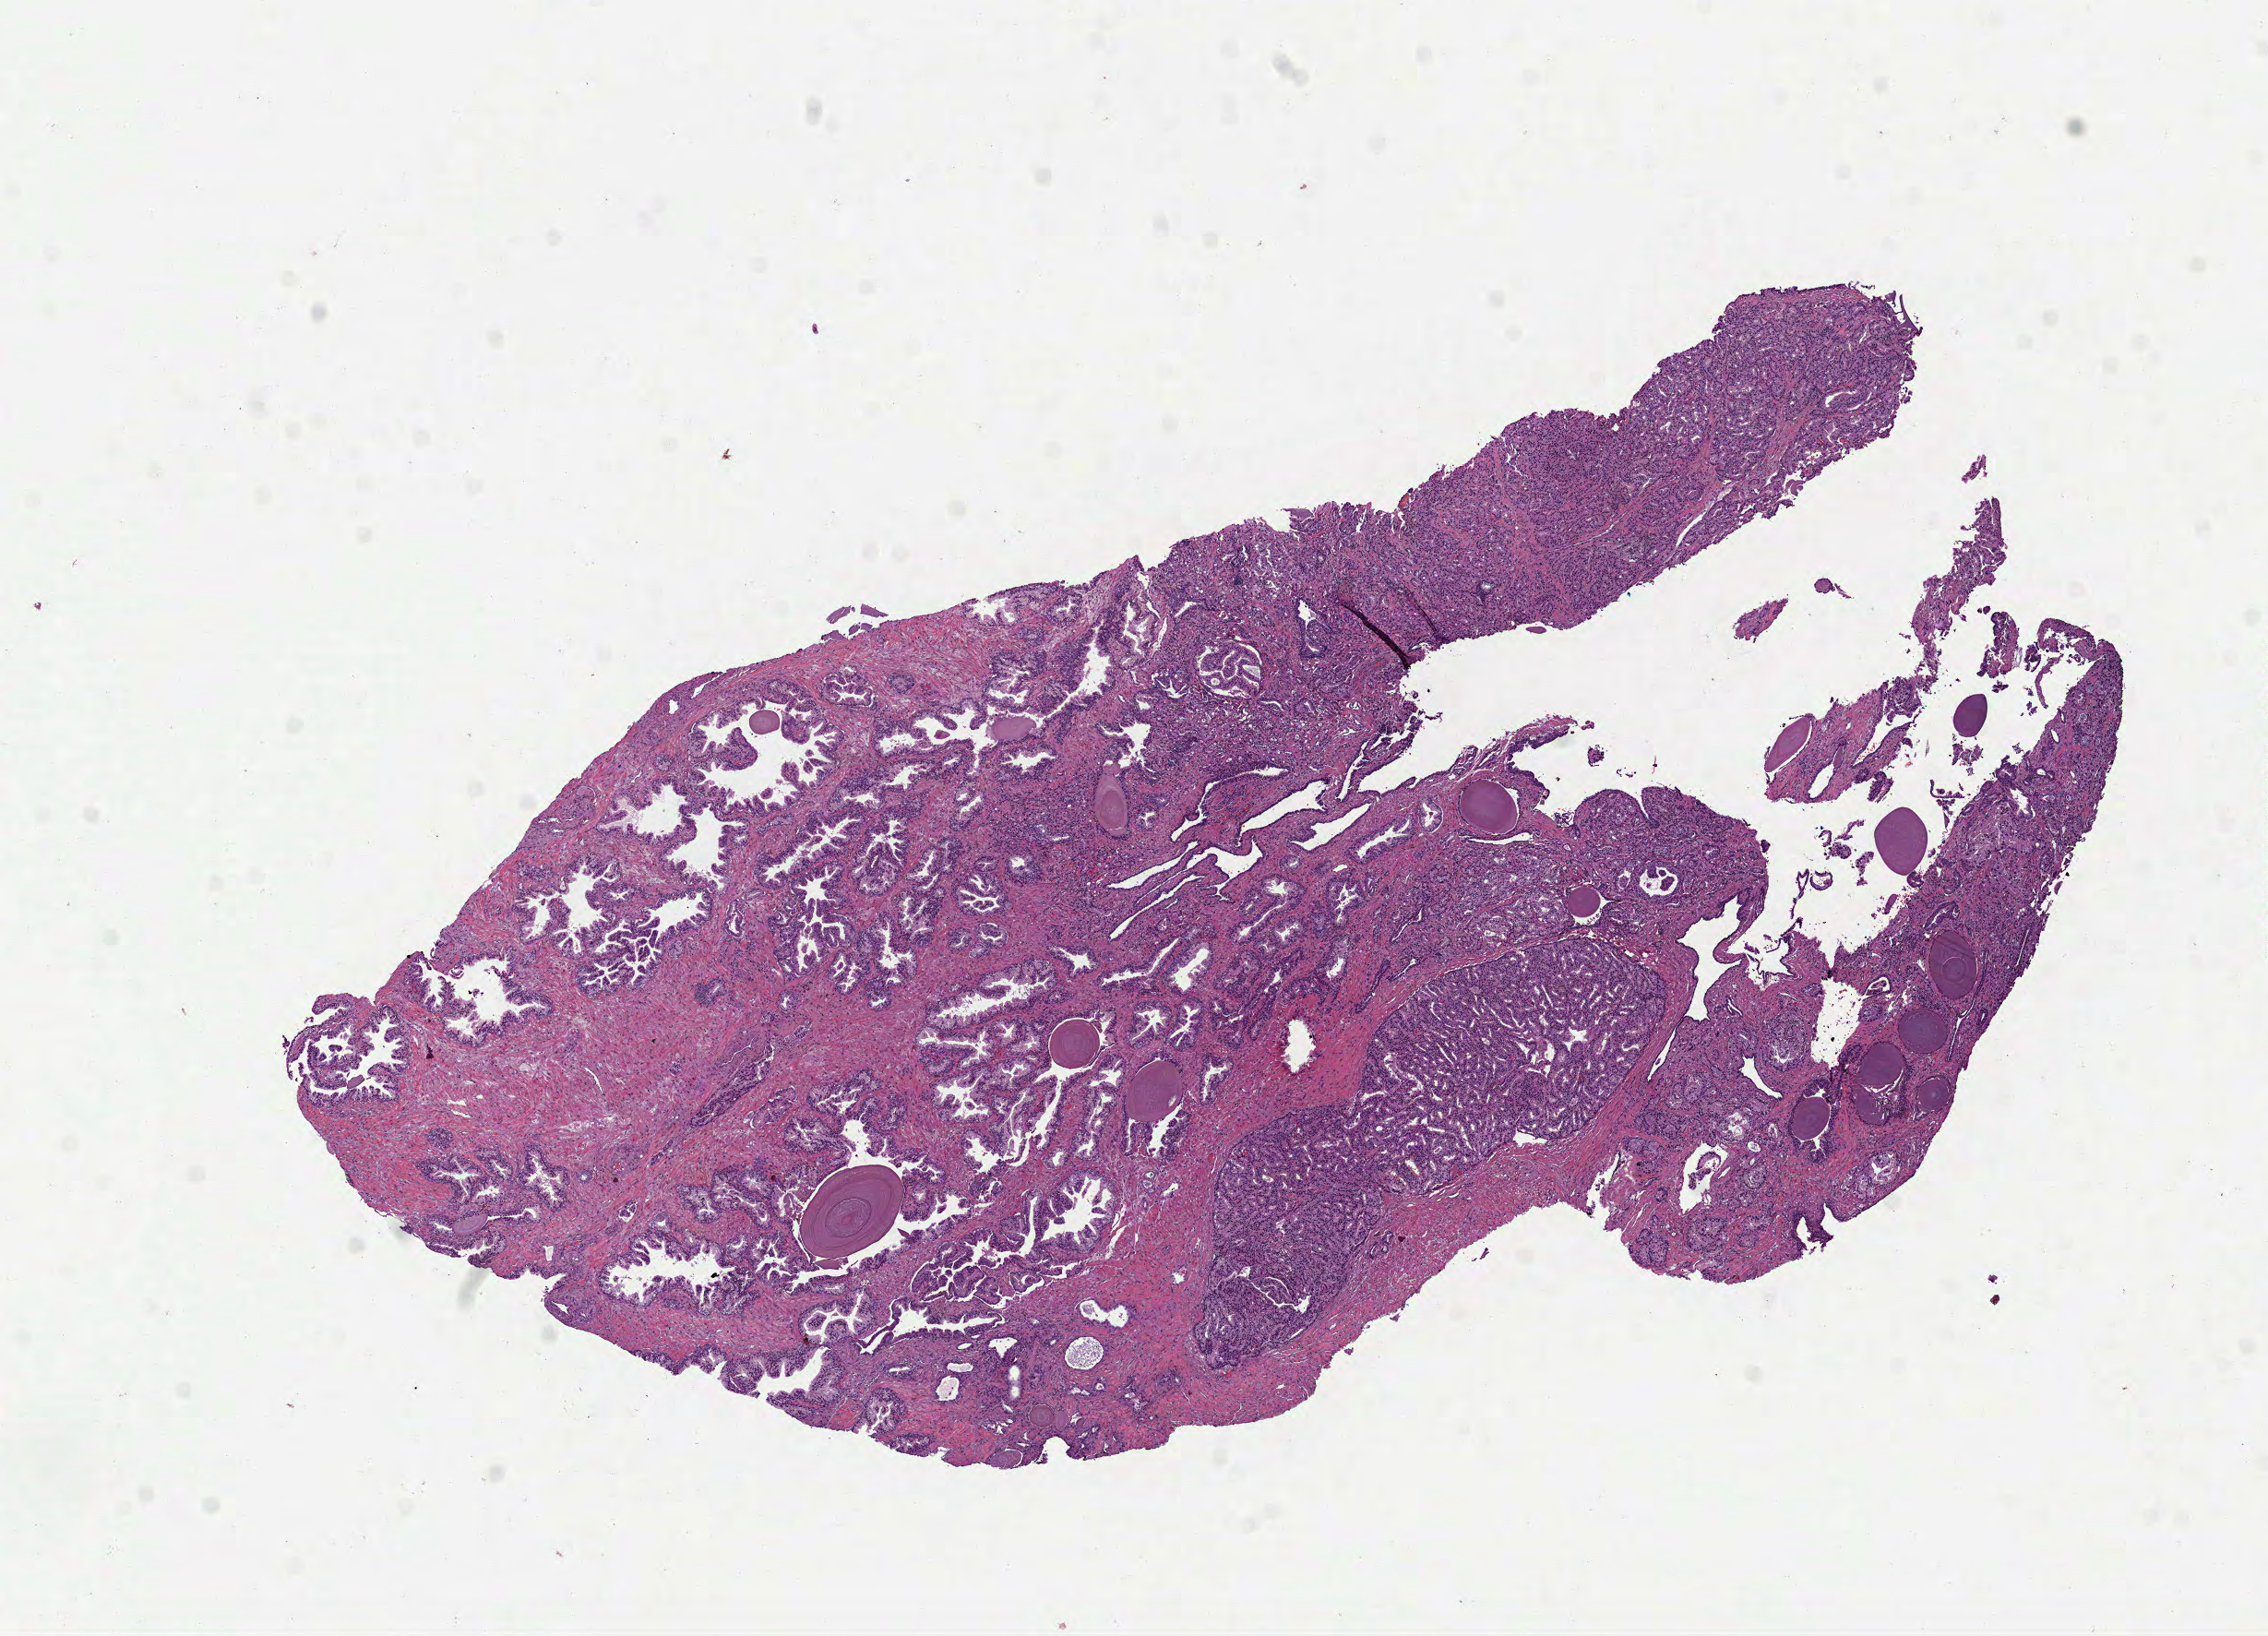
Whole-slide histology image, H&E-stained, low-resolution overview of the scanned area, about 9.9 x 7.1 mm (from a 40x scan); formalin-fixed paraffin-embedded (FFPE) diagnostic section; sample: primary tumour, prostate. Male patient; age at initial diagnosis 58 years. Gleason score: 7 (3+4).
- pathologic diagnosis: Adenocarcinoma, NOS